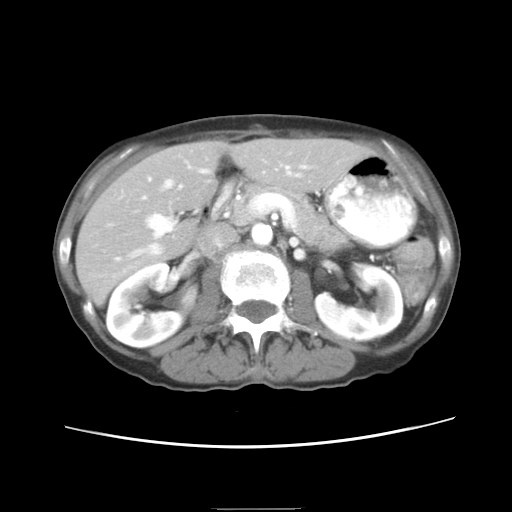
Contrast-enhanced abdominal CT, one axial slice; slice 10 of 26 in the series (ordered by position); reconstruction kernel STANDARD; 120 kVp; intravenous contrast given; soft-tissue window (W 400 / L 40 HU); 512 × 512 image matrix, field of view 340 × 340 mm. Female patient, age 65 years. From the clinical record (not read from this slice): diagnosis: colorectal cancer liver metastases, imaged before liver resection; multiple liver metastases: no; chemotherapy before resection: yes.
Annotated regions visible in this slice (outlined manually by an expert reader):
- hepatic veins: bounding box (x1, y1, x2, y2) in pixels: (129, 161, 308, 257)
- liver: (76, 140, 365, 303)
- planned liver remnant (the part of the liver to remain after resection): (78, 140, 365, 303)
- portal vein (with intrahepatic branches): (142, 165, 305, 254)